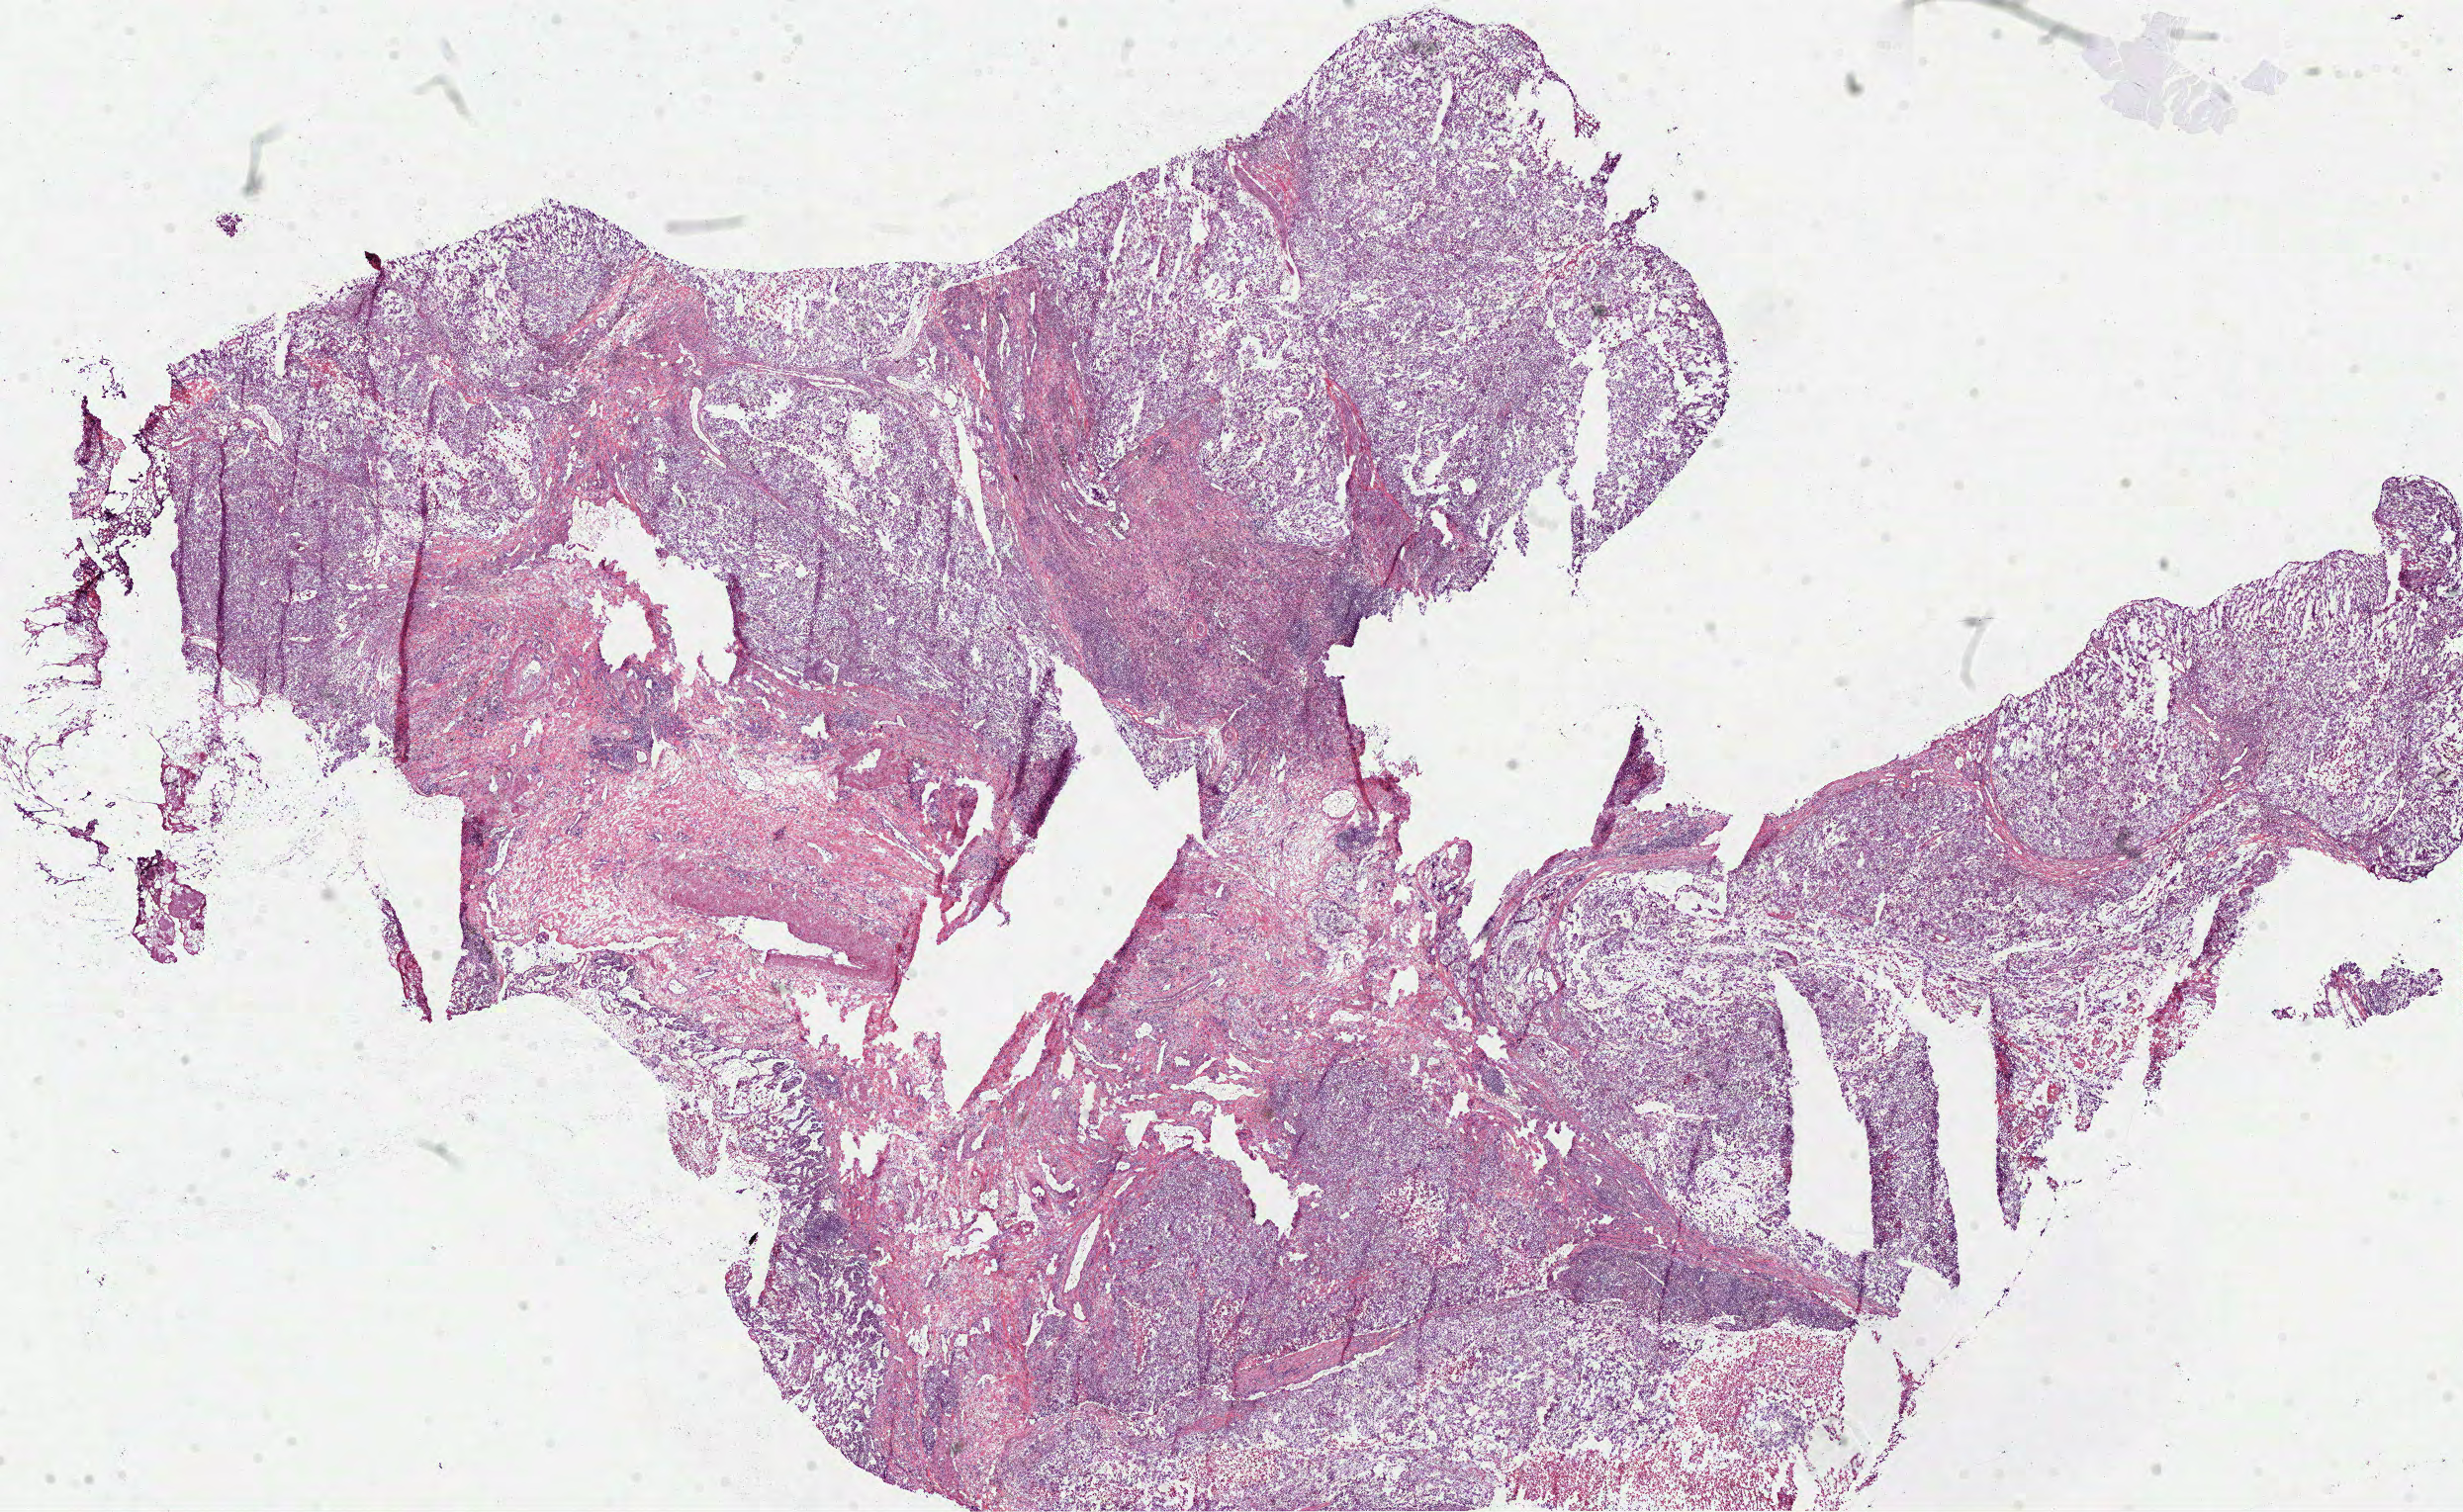
Whole-slide histology image, H&E-stained, a low-resolution overview of the entire scanned area, about 20.1 x 12.3 mm. Frozen section from the bottom of the tissue portion. Sample: primary tumour, lung. Patient: male, age at initial diagnosis 59 years. Pathologist review of this section (percent, as recorded): tumour cells 70%, tumour nuclei 80%, normal cells 0%, stromal cells 20%, necrosis 10%.
TNM: T1b N1 M0. Laterality: right. Diagnosis: Squamous cell carcinoma, NOS (upper lobe, lung). AJCC pathologic stage: IIA (7th edition).